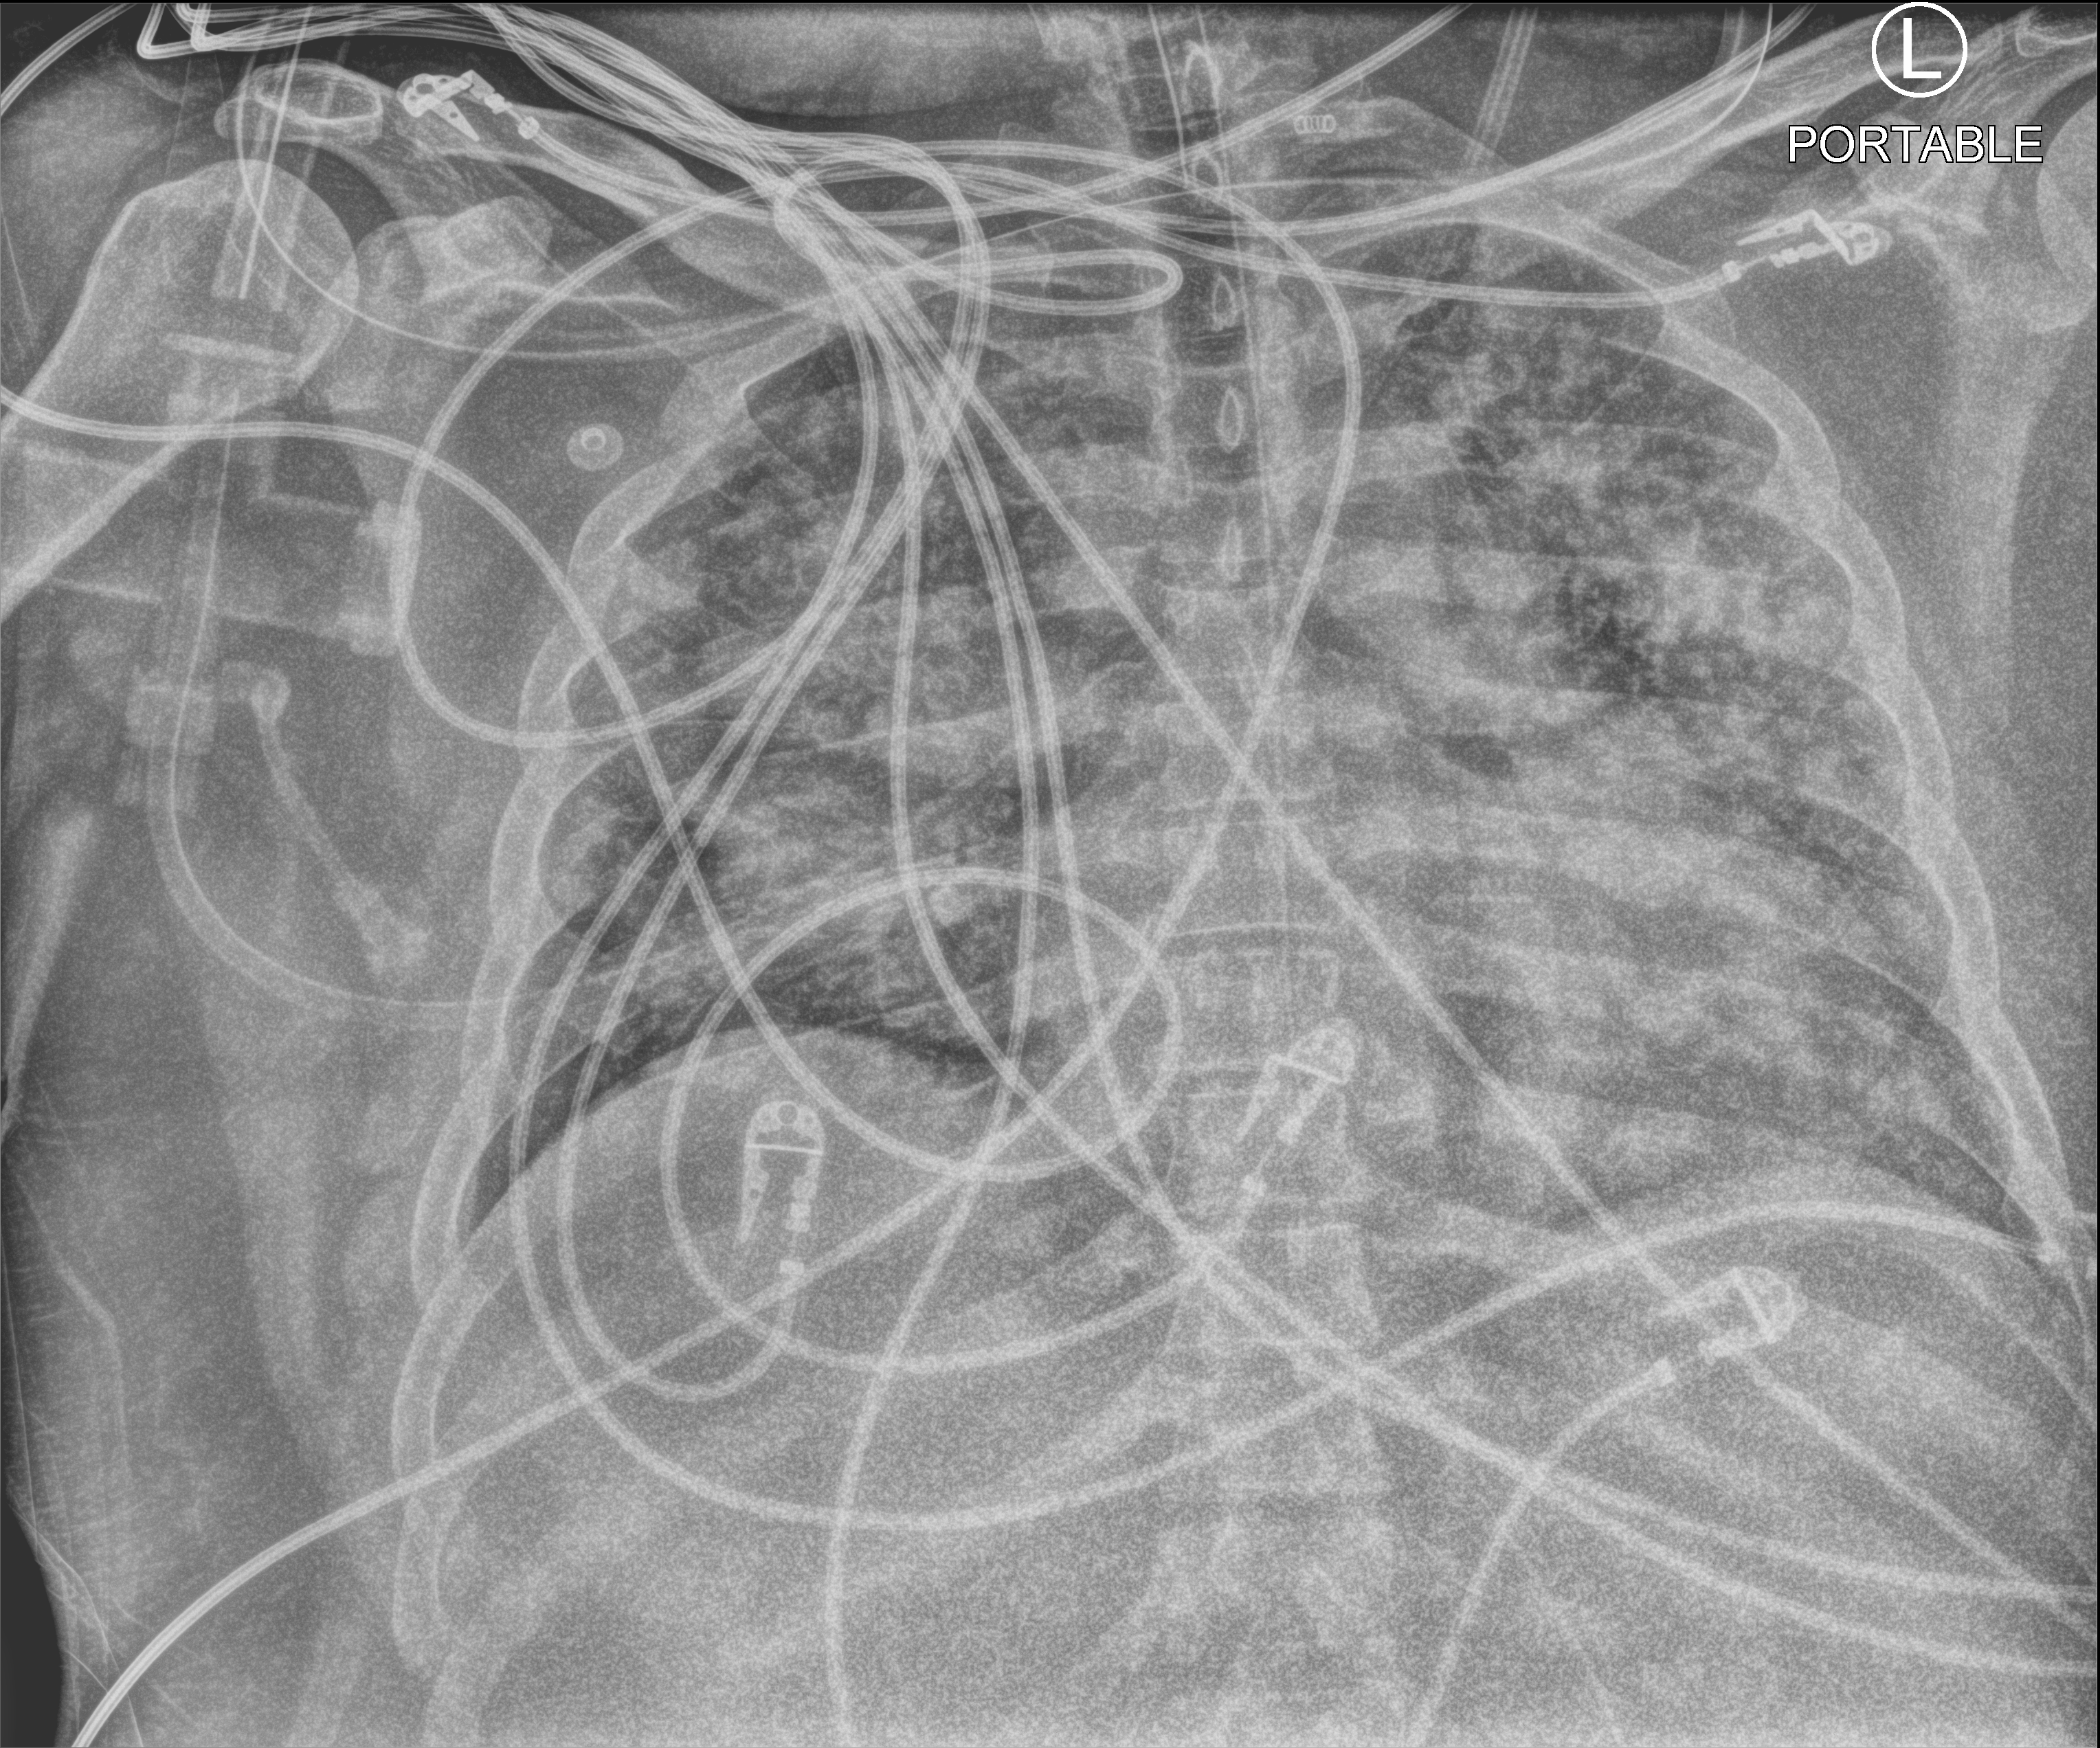
Bedside chest radiograph (computed radiography). Patient hospitalised with COVID-19, aged 18–59 years.
Admission-level facts for this patient (not findings on this image; timing relative to this image not recorded):
- mechanically ventilated during this hospital stay: yes
- length of hospital stay: 22 days
- admitted to intensive care during this hospital stay: yes